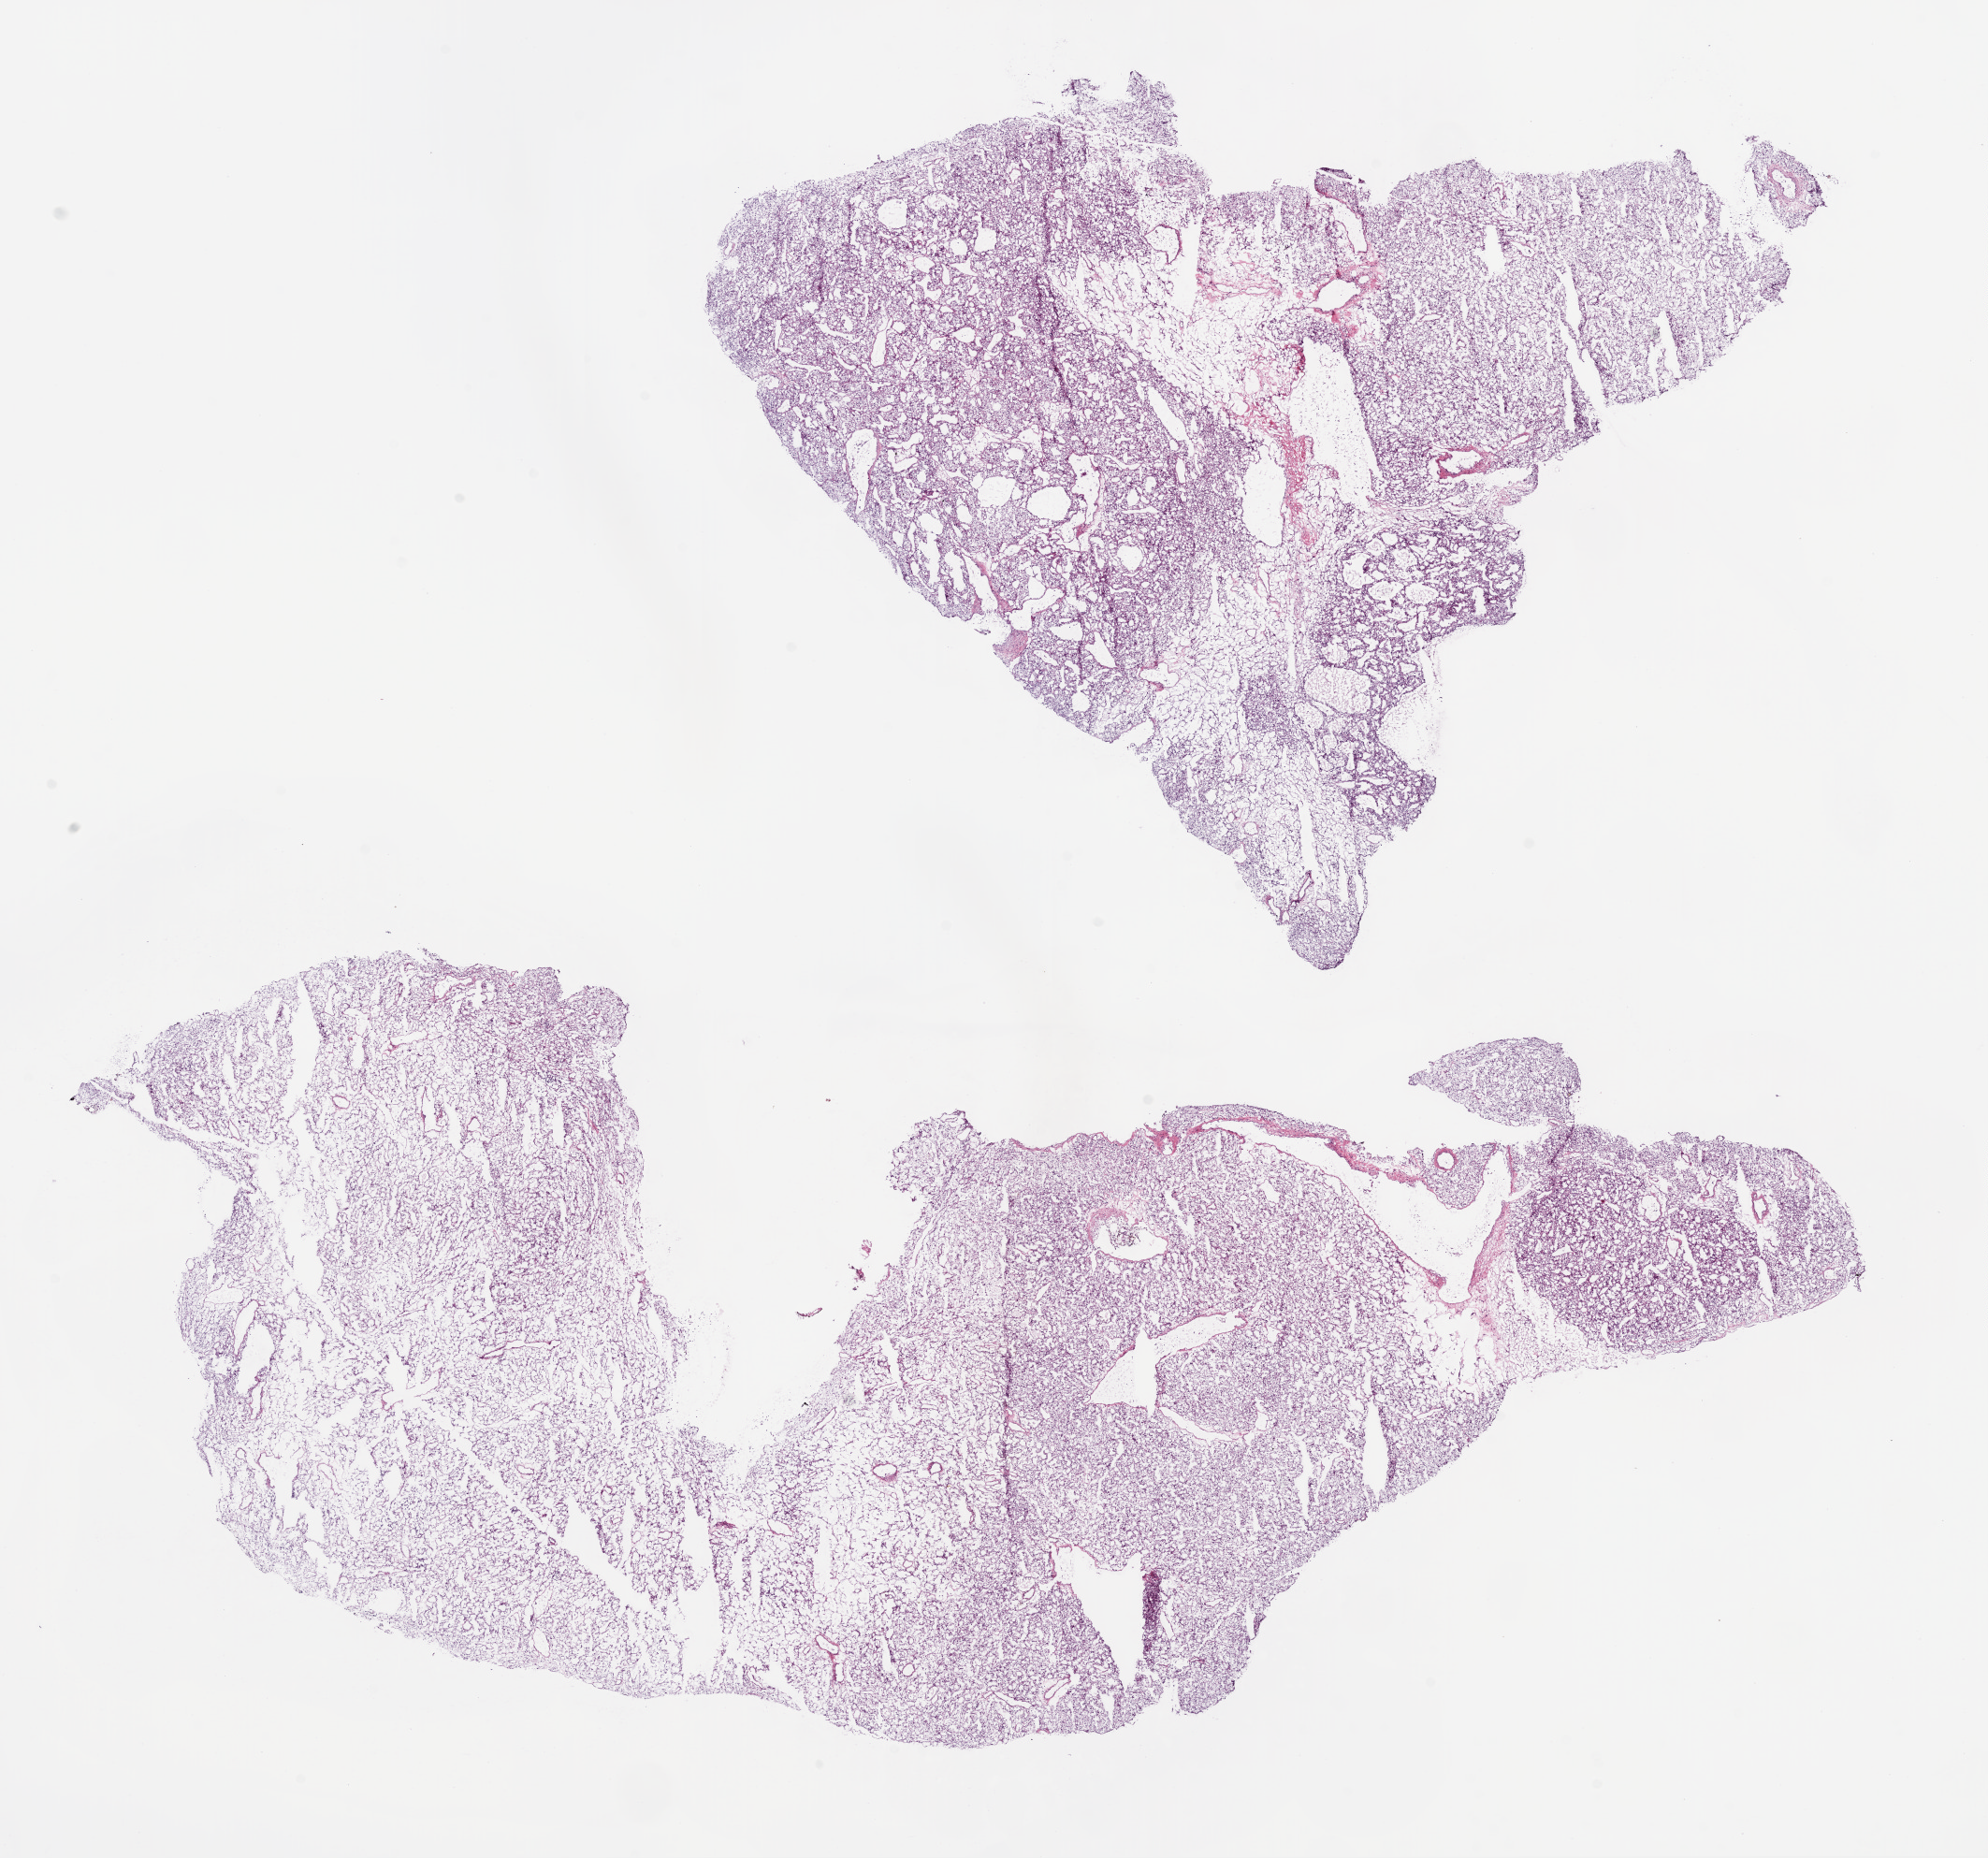
Whole-slide histology image, H&E-stained, whole scanned area (about 17.1 x 15.9 mm) shown as a low-resolution overview. Frozen section from the bottom of the tissue portion. Kidney, primary tumour sample. Male, age 75 years at initial diagnosis. Composition of this section per pathologist review: tumour cells 90%, tumour nuclei 90%.
Pathologic diagnosis: Clear cell adenocarcinoma, NOS.